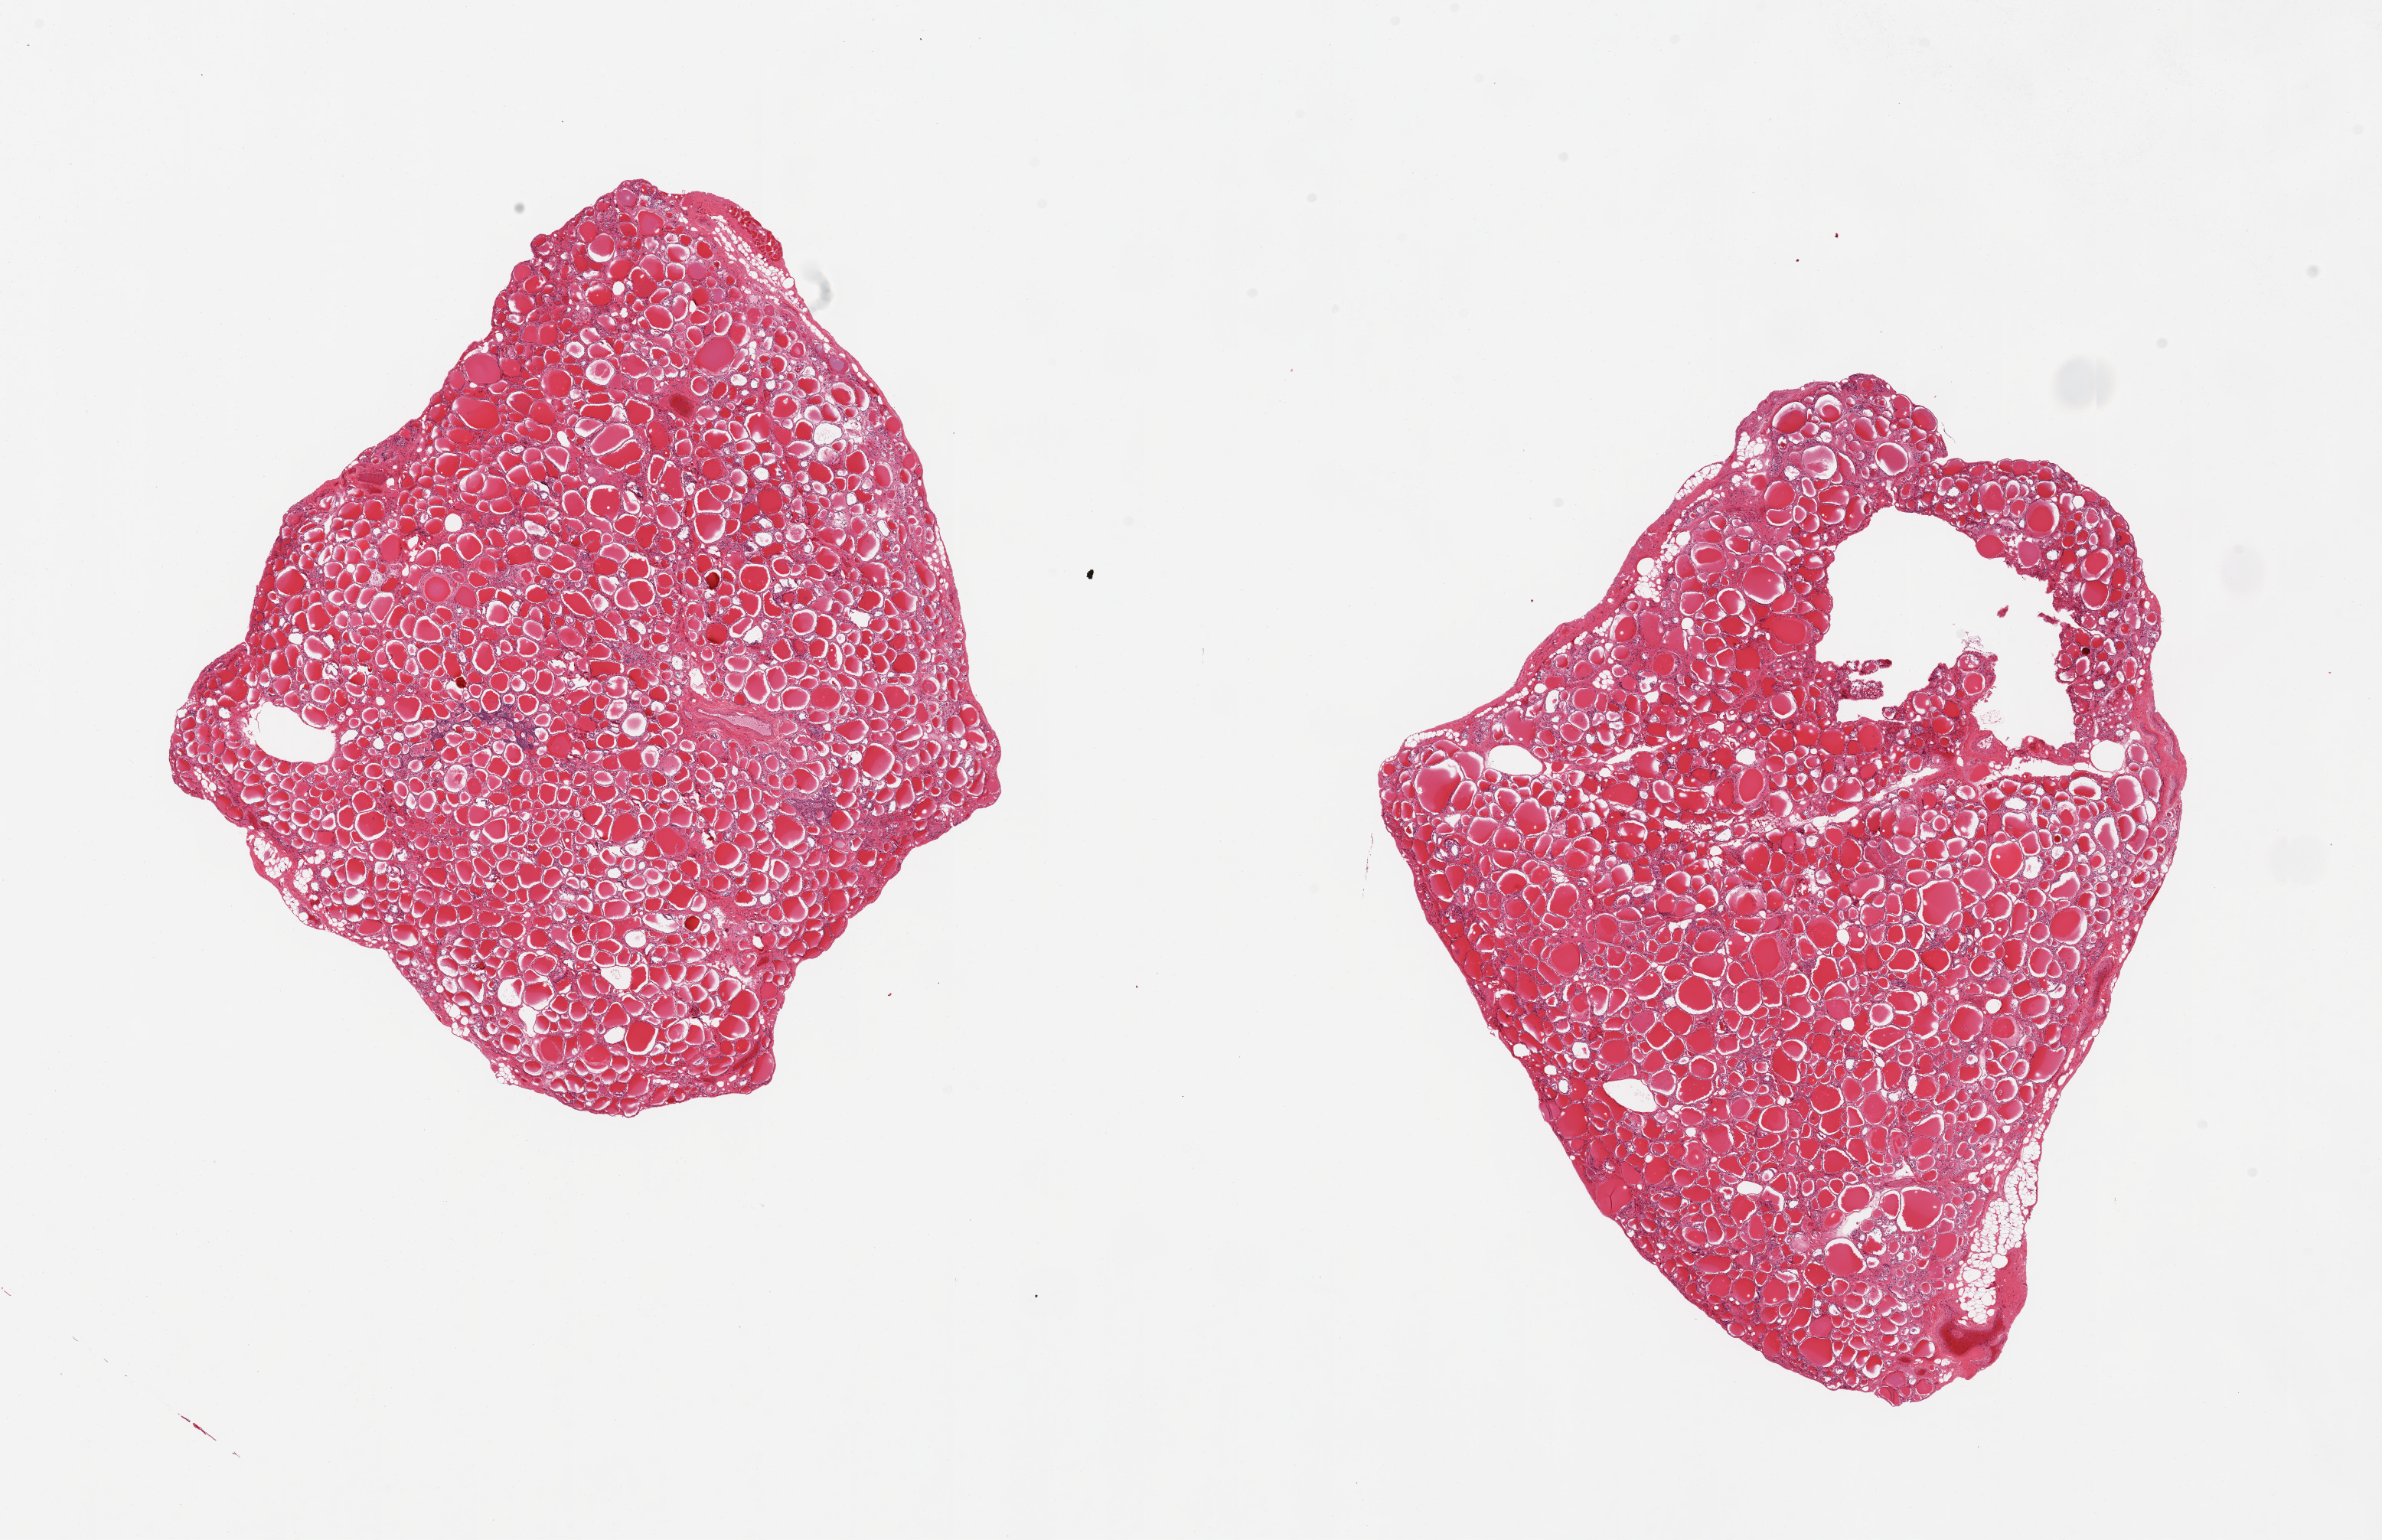
Hematoxylin and eosin (H&E) whole-slide image — shown as a low-resolution overview of the whole scanned area (about 24.6 x 15.9 mm), PAXgene-fixed, paraffin-embedded tissue, section of thyroid (target tissue), tissue donor sample. Donor: male.
Reviewer comment on this tissue sample: 2 pieces; thyroid with small portion of attached fat and skeletal muscle, few solid cell nests.